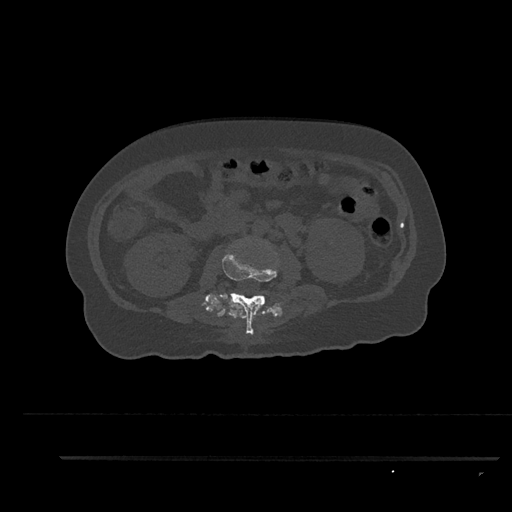
CT including the spine, one axial slice. Reconstruction kernel Br40s/3. Bone window (W 1800 / L 400 HU). 0.5 mm slice thickness. 512 × 512 image matrix. Patient: female, 44 years. Case-level facts recorded for this patient, not image findings: primary cancer: renal.
Outlined on this slice (semi-automatic segmentation, software-assisted and operator-edited):
- L2 vertebra: bounding box <222,250,277,335> (left, top, right, bottom; pixels)